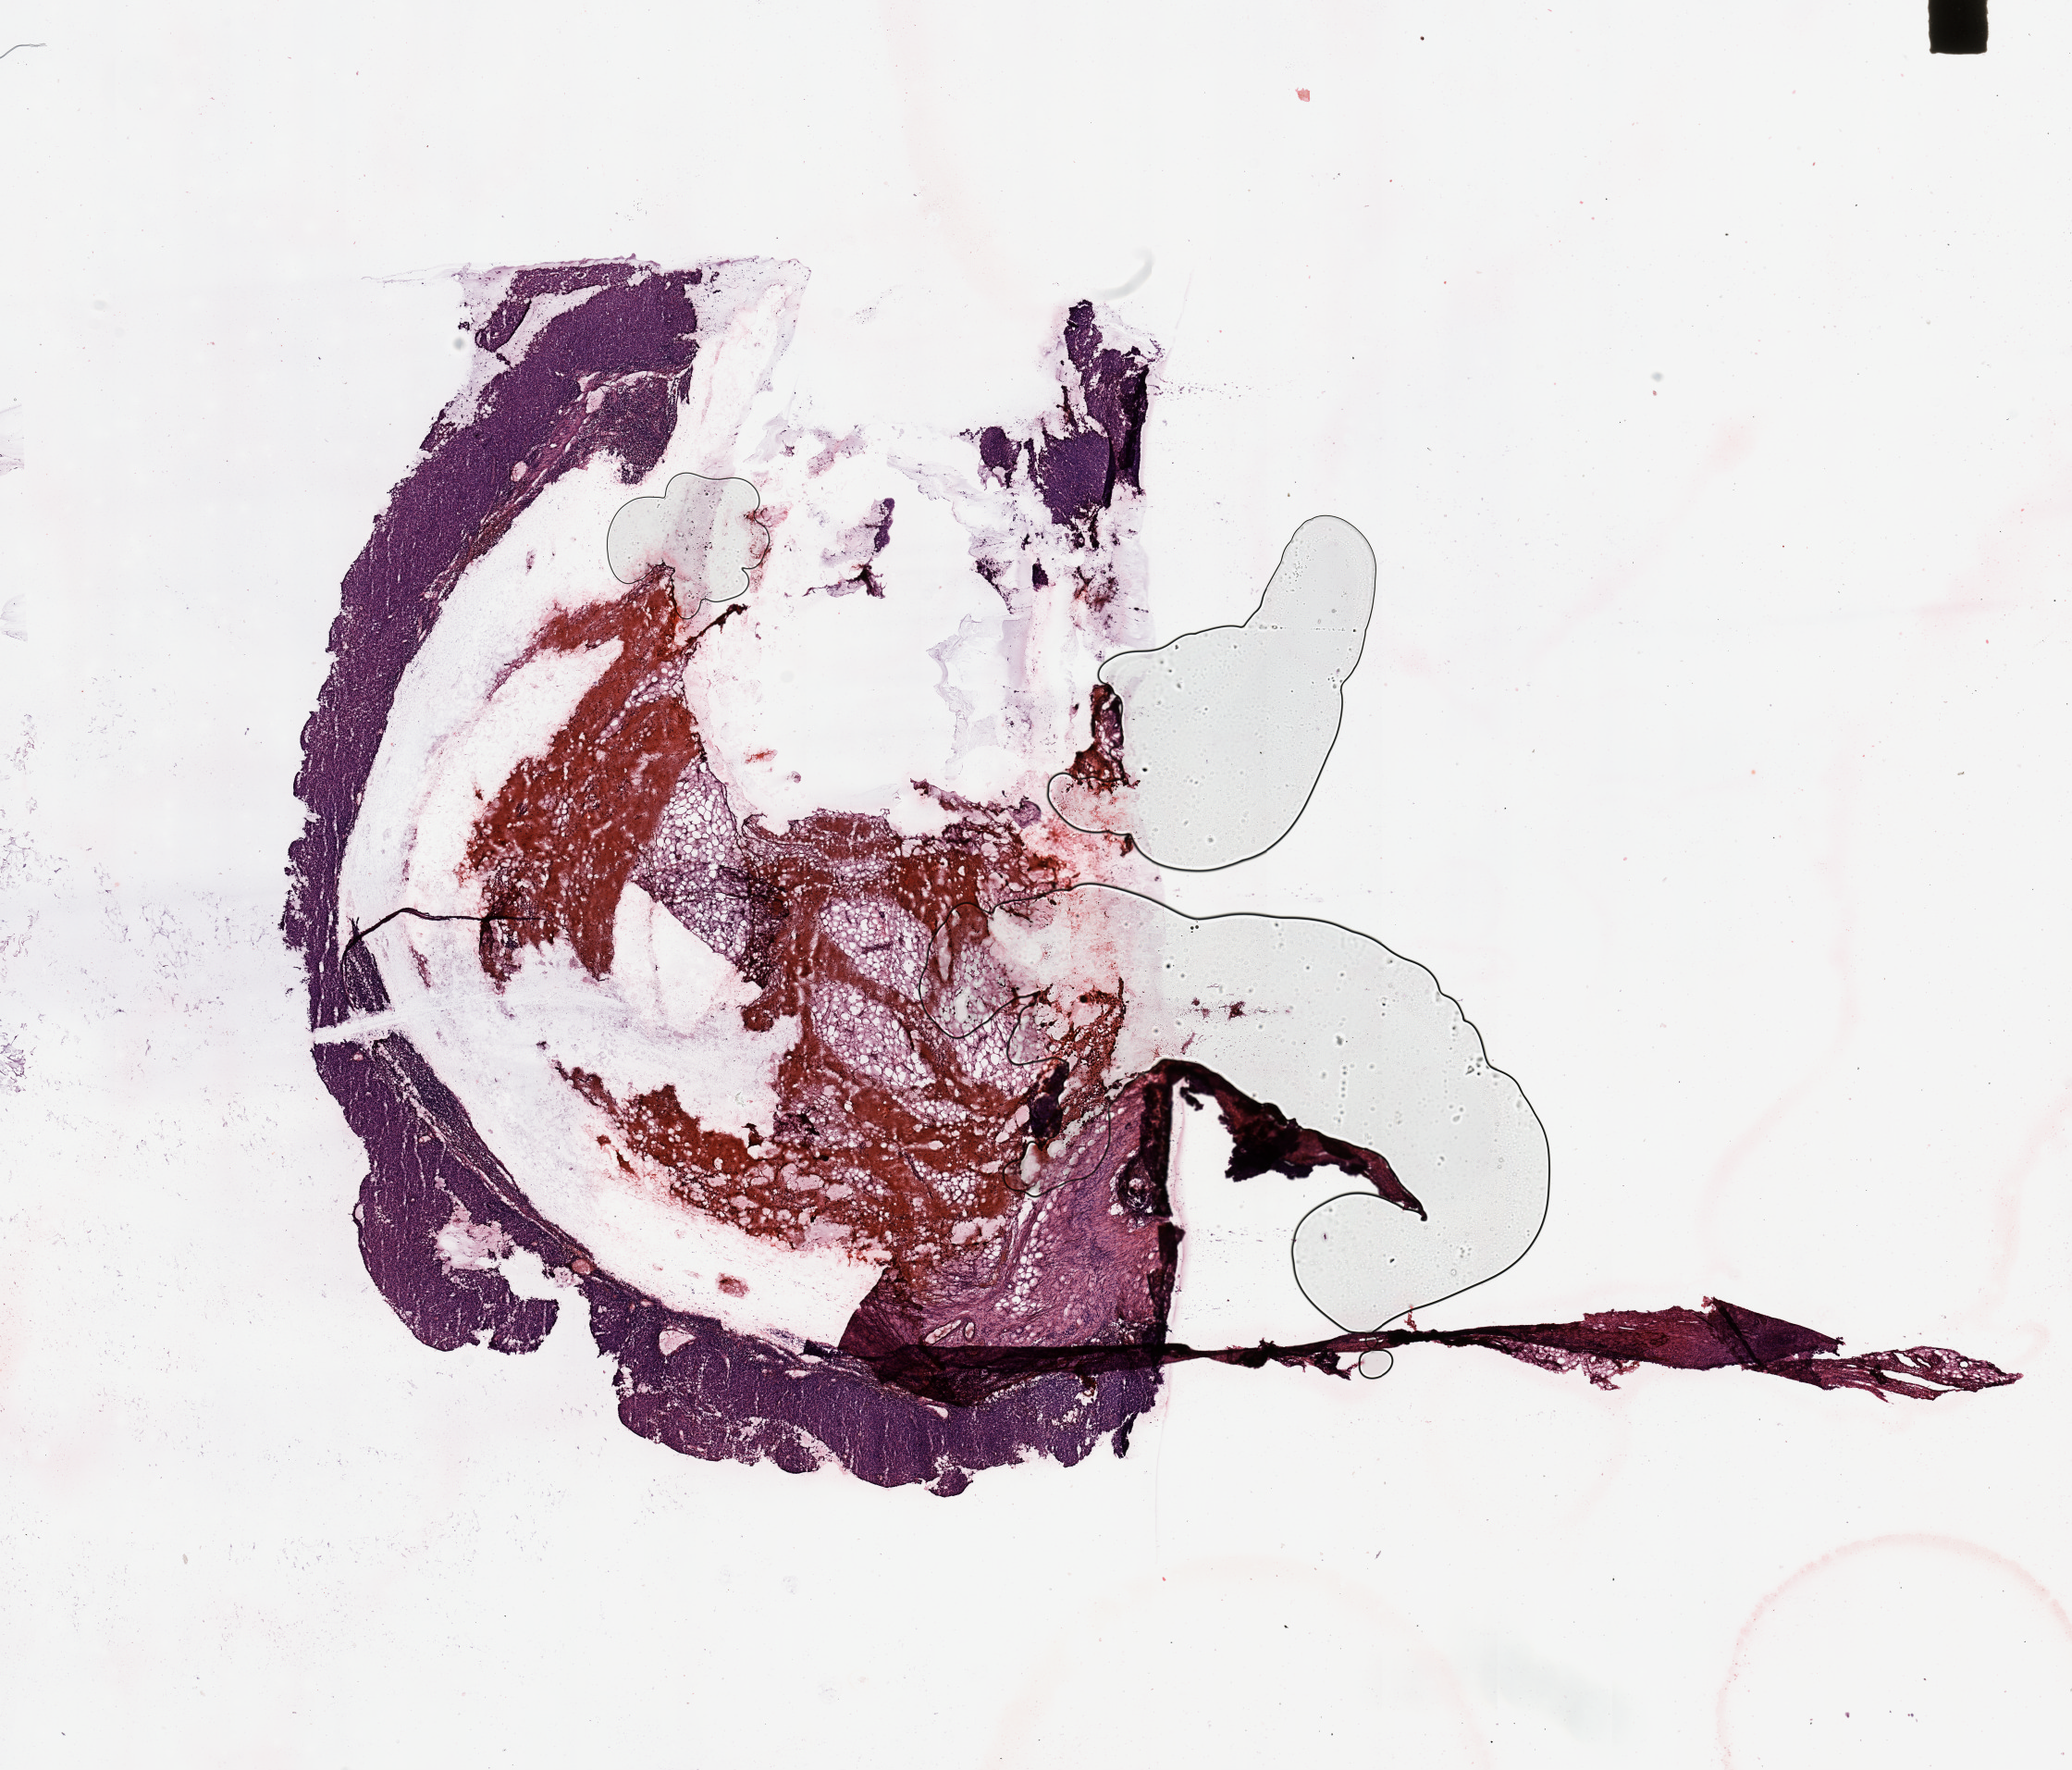
Digitized H&E-stained tissue section (whole slide) — whole scanned area (about 17.7 x 15.1 mm, from a 20x scan) shown as a low-resolution overview; melanoma tumour tissue; sampled site not recorded. 66-year-old male patient.
• patient diagnosis (cohort enrolment): cutaneous melanoma (skin)